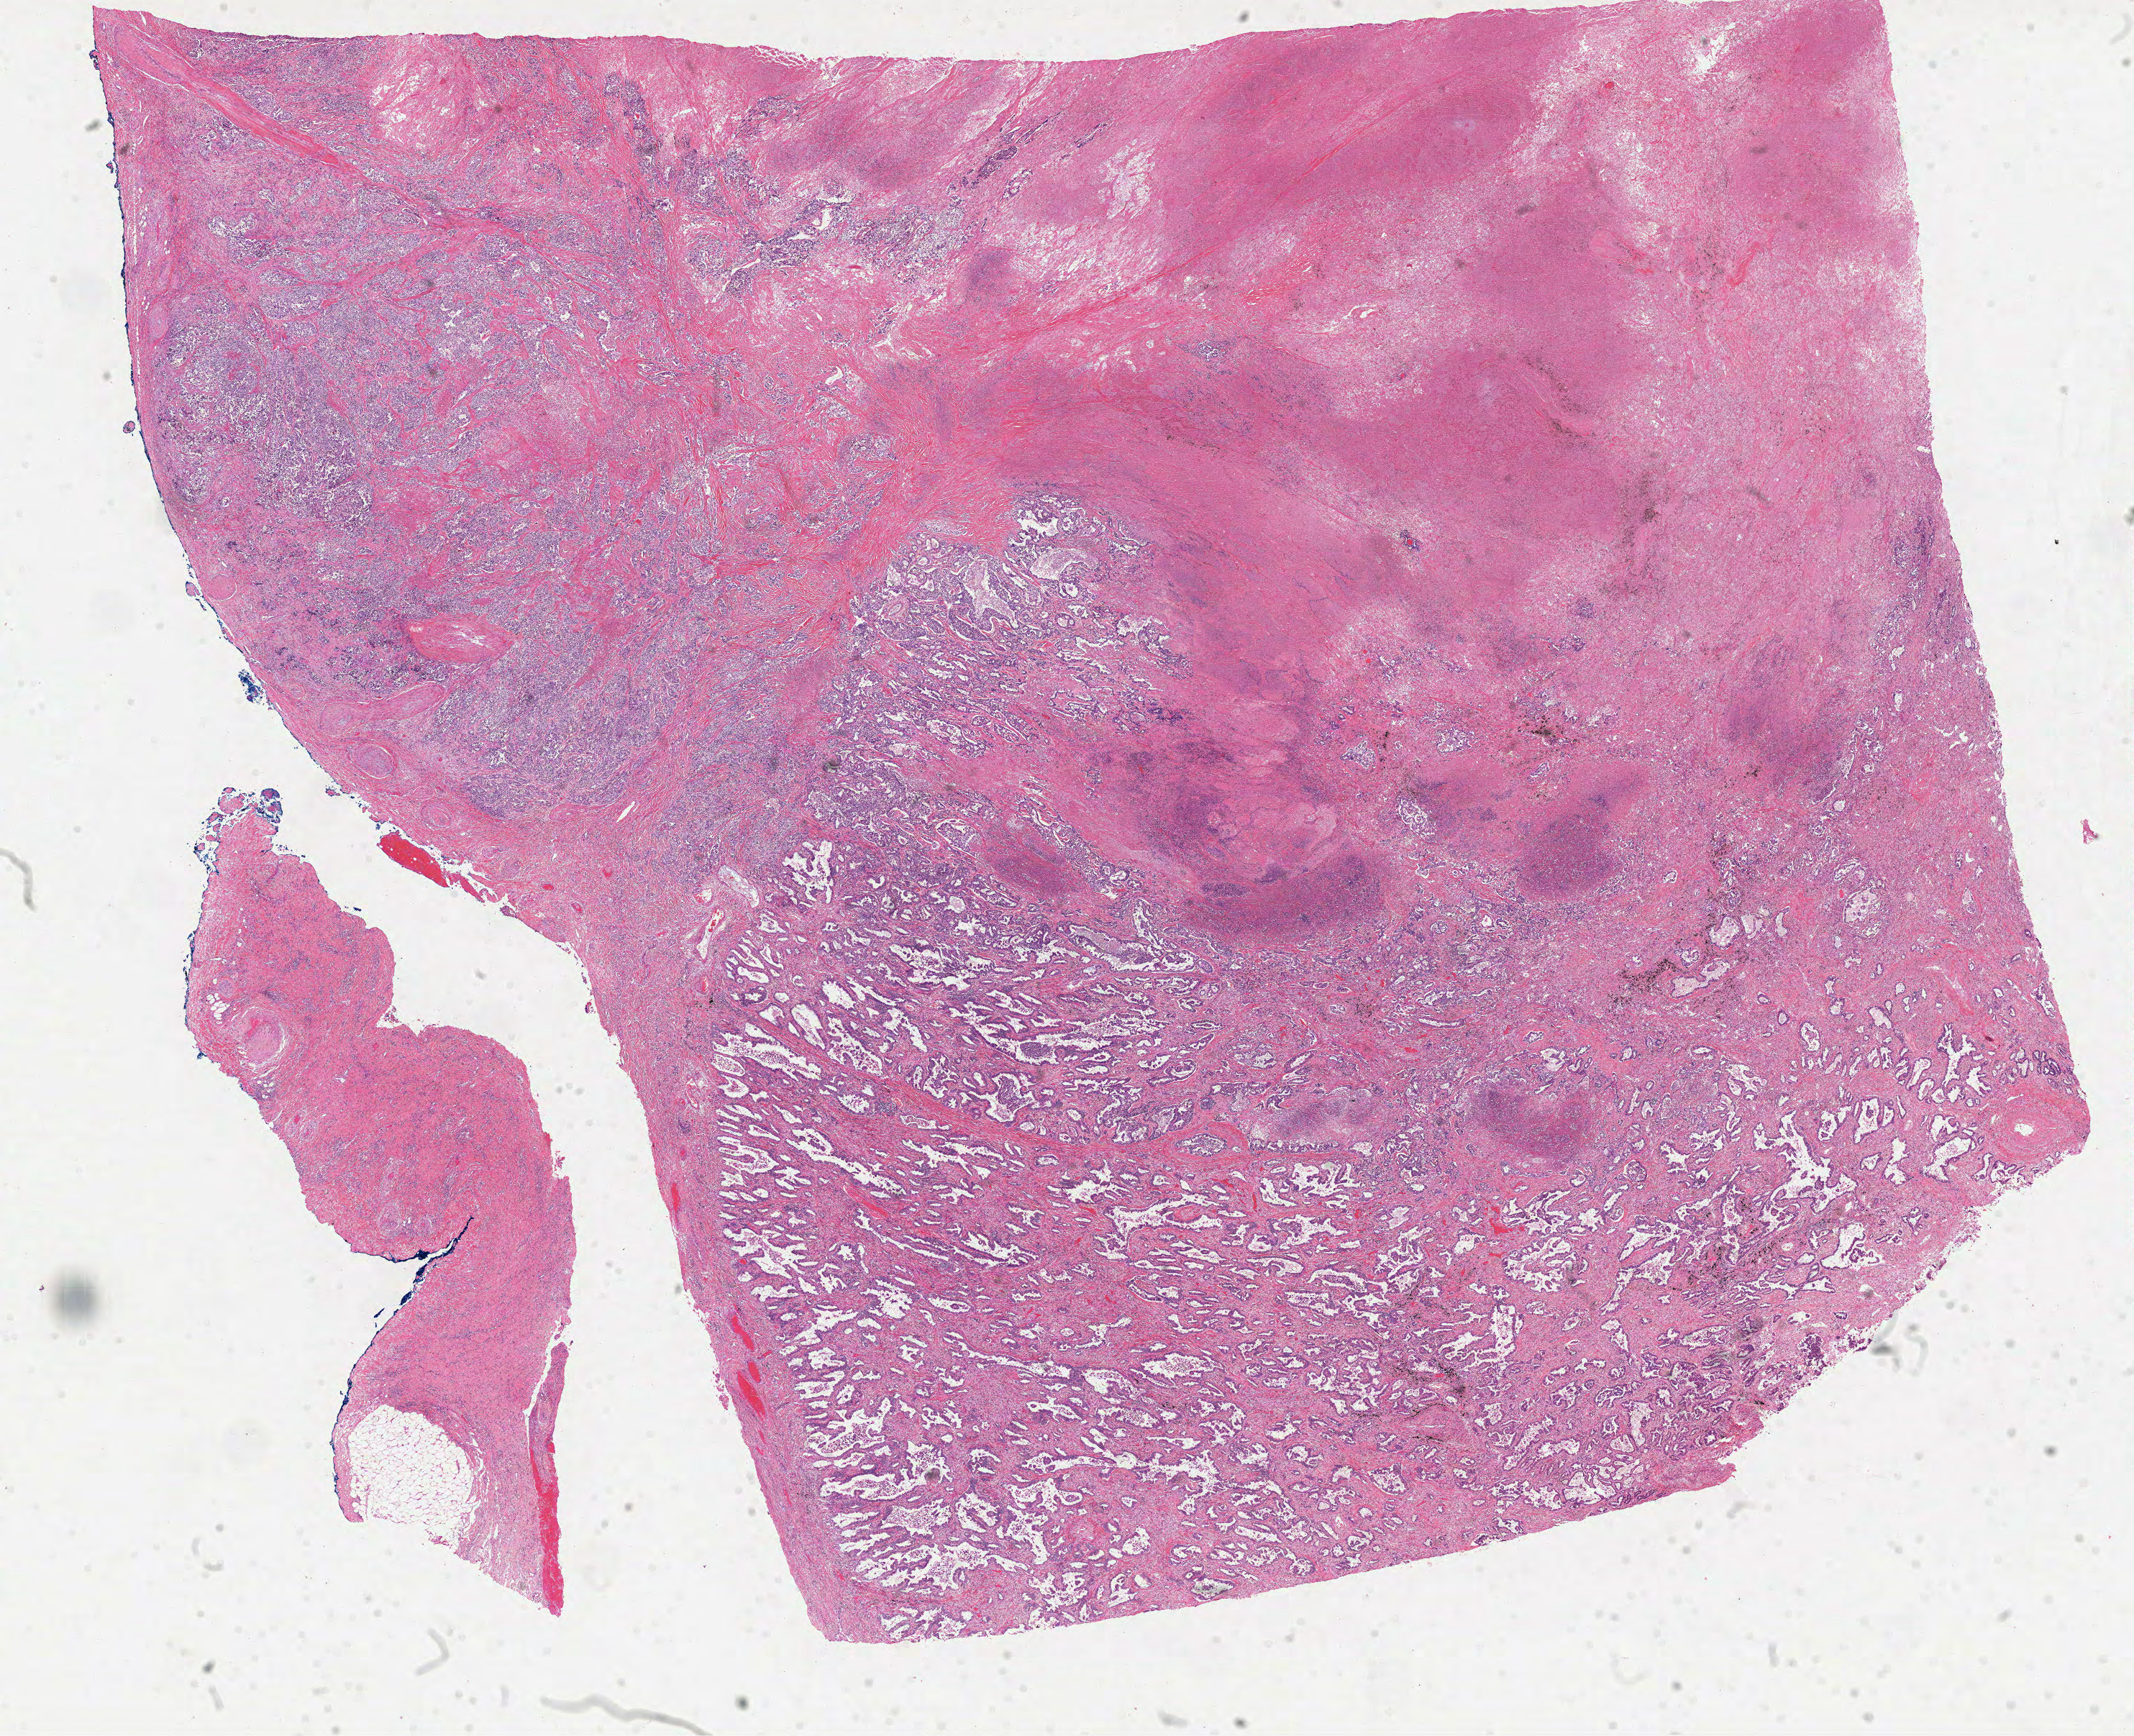
H&E whole-slide image, whole scanned area (about 23.9 x 19.5 mm) shown as a low-resolution overview, FFPE section, sample: primary tumour, lung. Patient: female, age at initial diagnosis 69 years.
Pathologic diagnosis: Adenocarcinoma with mixed subtypes. Laterality: left. AJCC pathologic stage: IIB (7th edition).